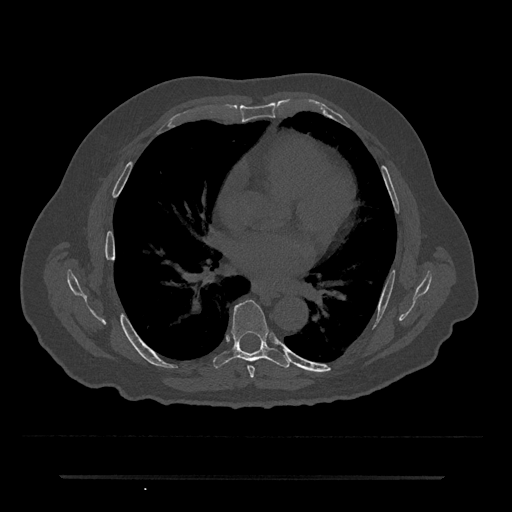
CT including the spine, one axial slice; position 395 of 797 along the scan axis; reconstruction kernel Br40s/3; 120 kVp; bone window (W 1800 / L 400 HU); 0.5 mm slice thickness; 512 × 512 image matrix. Male patient, age 69 years. Case-level facts recorded for this patient, not image findings: primary cancer: prostate.
Annotated regions visible in this slice (semi-automatic segmentation, software-assisted and operator-edited):
- T6 vertebra: box from (x=248, y=365) to (x=255, y=378) px
- T7 vertebra: (x=213, y=299)–(x=290, y=368)